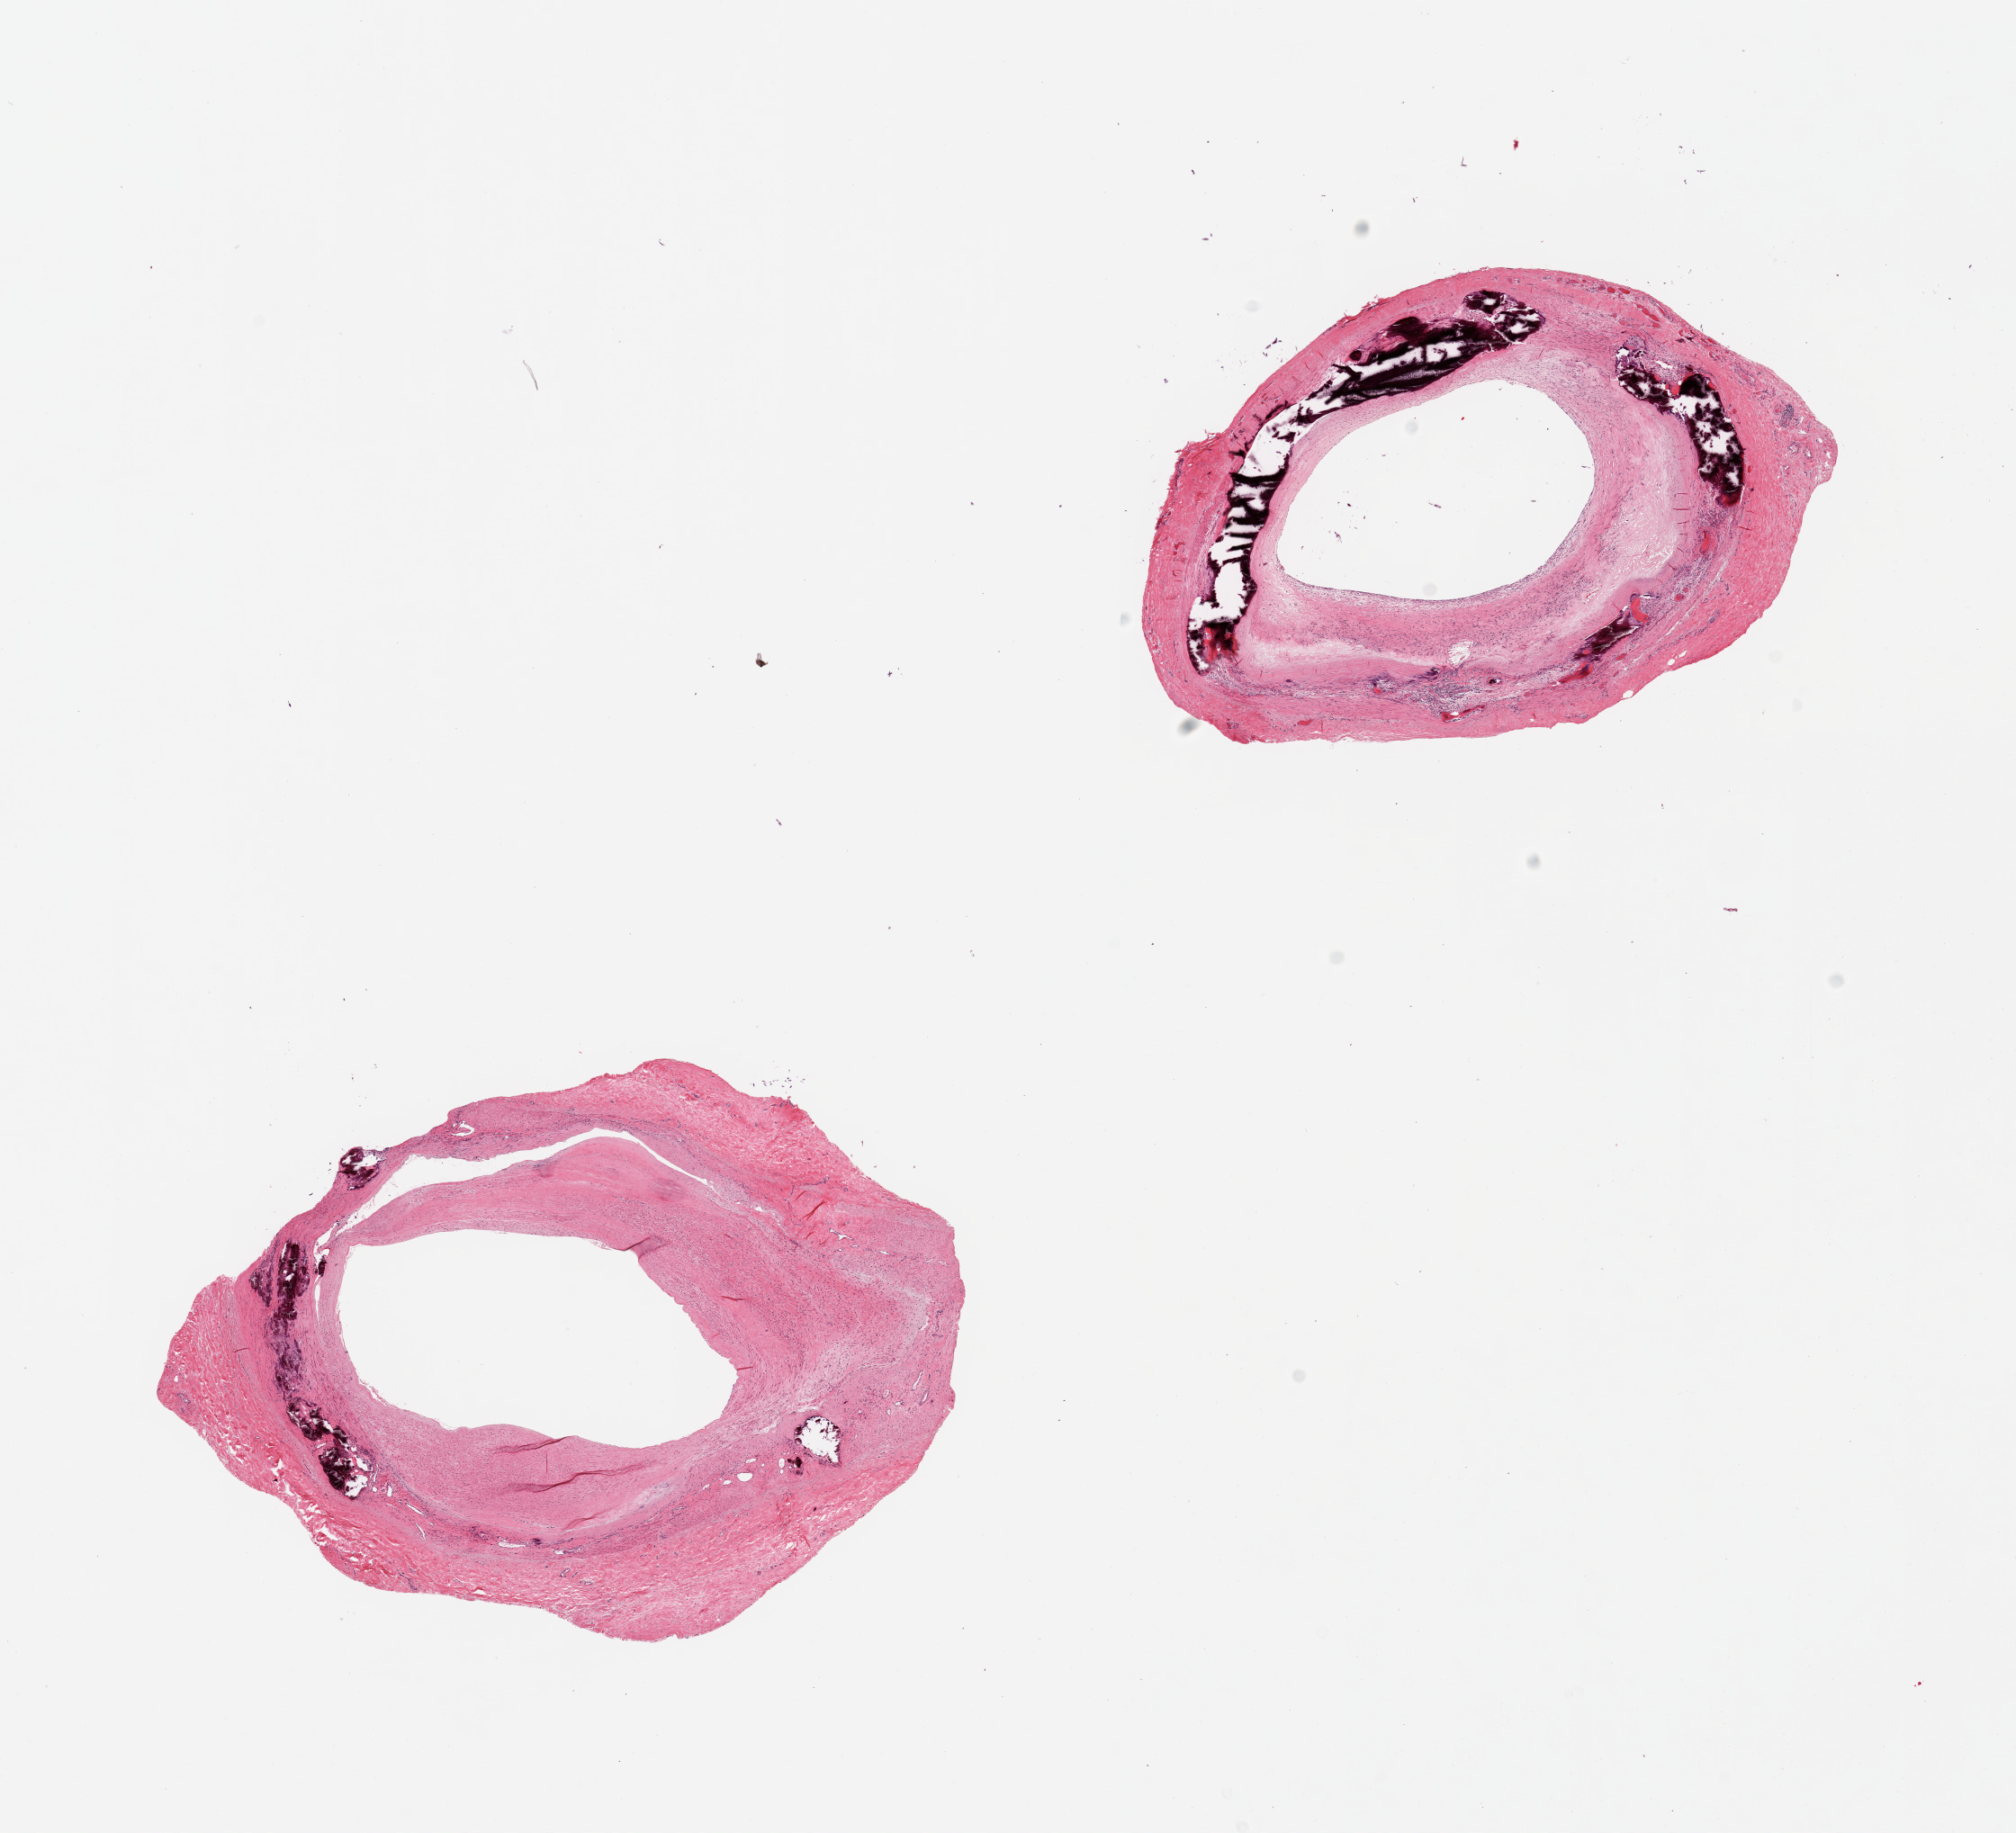
Whole-slide image, H&E stain — low-resolution overview of the scanned area, about 17.7 x 16.1 mm (from a 20x scan), PAXgene-fixed paraffin-embedded (PFPE) section, section of tibial artery (target tissue), donor tissue sample. Donor sex: male.
- pathologist's review note for this sample: 2 pieces; medial calcification and calcific atherosclerosis with ossification